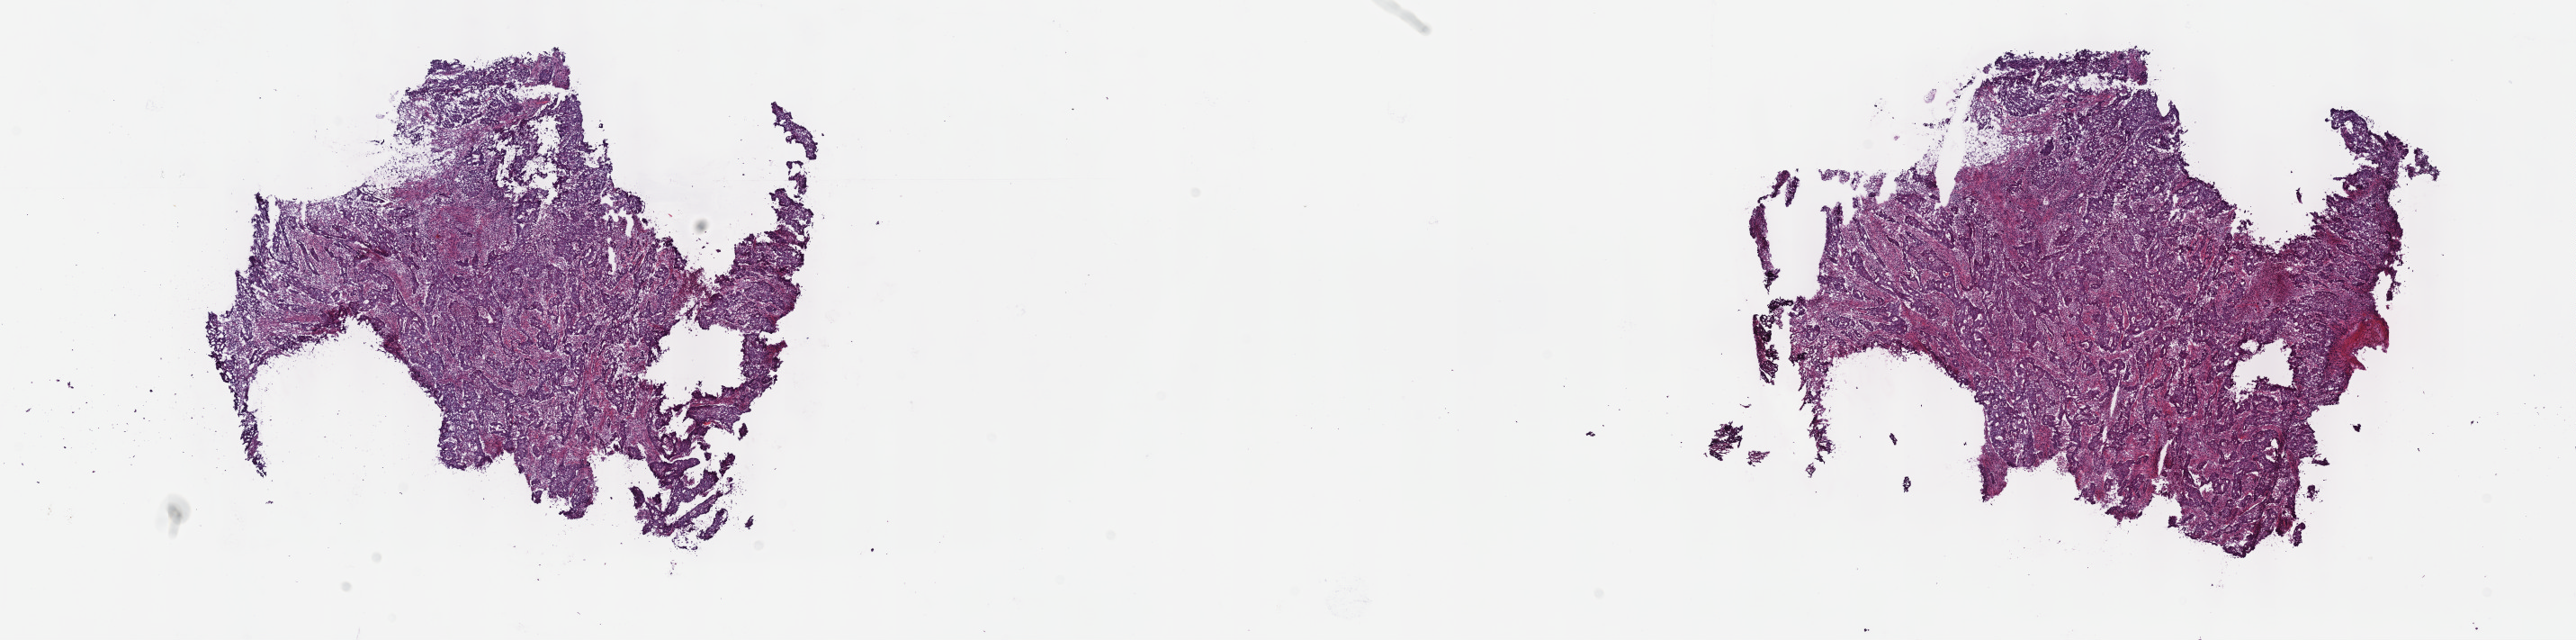
H&E-stained whole-slide image — low-resolution overview of the scanned area, about 23.2 x 5.8 mm. Frozen section. Primary tumour sample from the stomach. Patient: male, age at initial diagnosis 67 years. Histologic grade: G3 (poorly differentiated). Slide review estimates, as recorded: tumour cells 50%, tumour nuclei 60%, normal cells 0%, stromal cells 50%, necrosis 0%. Inflammatory infiltration, as recorded: lymphocyte infiltration 0%, monocyte infiltration 0%, neutrophil infiltration 0%.
AJCC pathologic stage: IIA. Histologic diagnosis: Adenocarcinoma, intestinal type (body of stomach). Lymph nodes positive (case pathology): 0 of 34 examined.